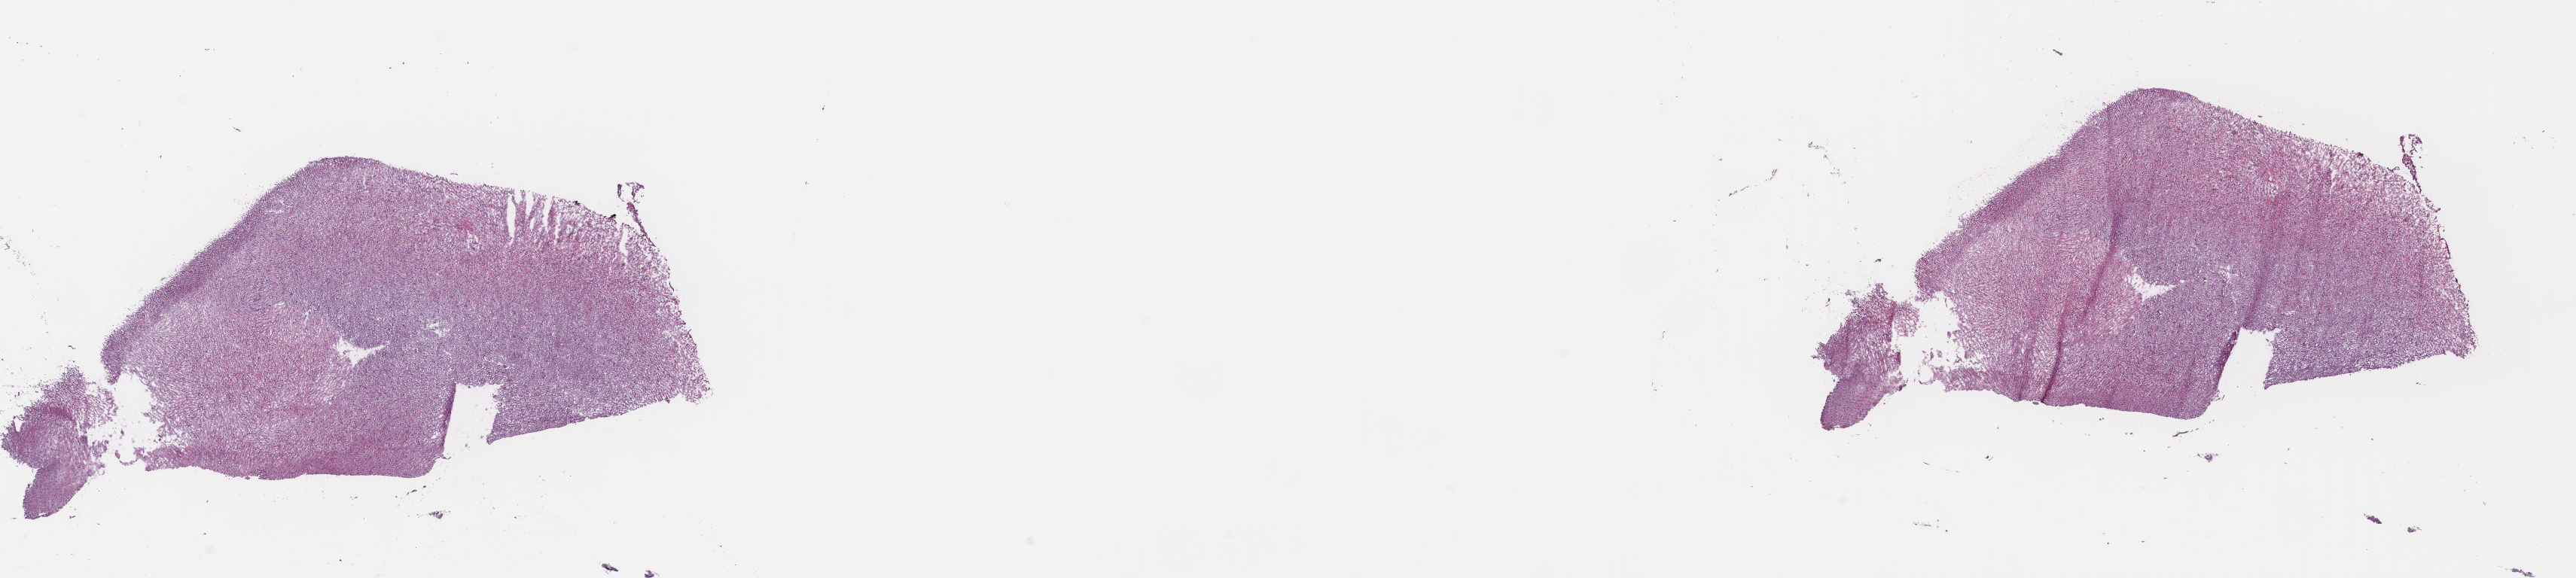
Digitized Hematoxylin and eosin (H&E) stained tissue section (whole slide) — low-resolution overview of the scanned area, about 26.9 x 6.0 mm, frozen section, sample: primary tumour, brain. Patient: female, age at initial diagnosis 38 years. Histologic grade: G2 (moderately differentiated). Slide review estimates, as recorded: tumour cells 65%, tumour nuclei 80%, normal cells 15%, stromal cells 20%, necrosis 0%. Infiltration values recorded for this section: lymphocyte infiltration 0%, monocyte infiltration 0%, neutrophil infiltration 0%.
Histologic diagnosis: Mixed glioma.